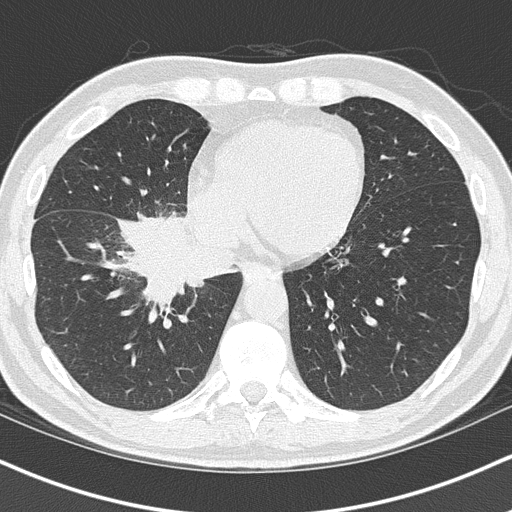
Low-dose screening chest CT, one axial slice. Position 43 of 151 along the scan axis. Reconstruction kernel B50f. 120 kVp. Lung window (W 1500 / L -600 HU). 512 × 512 image matrix.
Outlined on this slice (outlined manually by an expert reader):
- lesion 1 (tumor, hilum of right lung): bounding box [x1, y1, x2, y2] px = [123, 218, 192, 303]